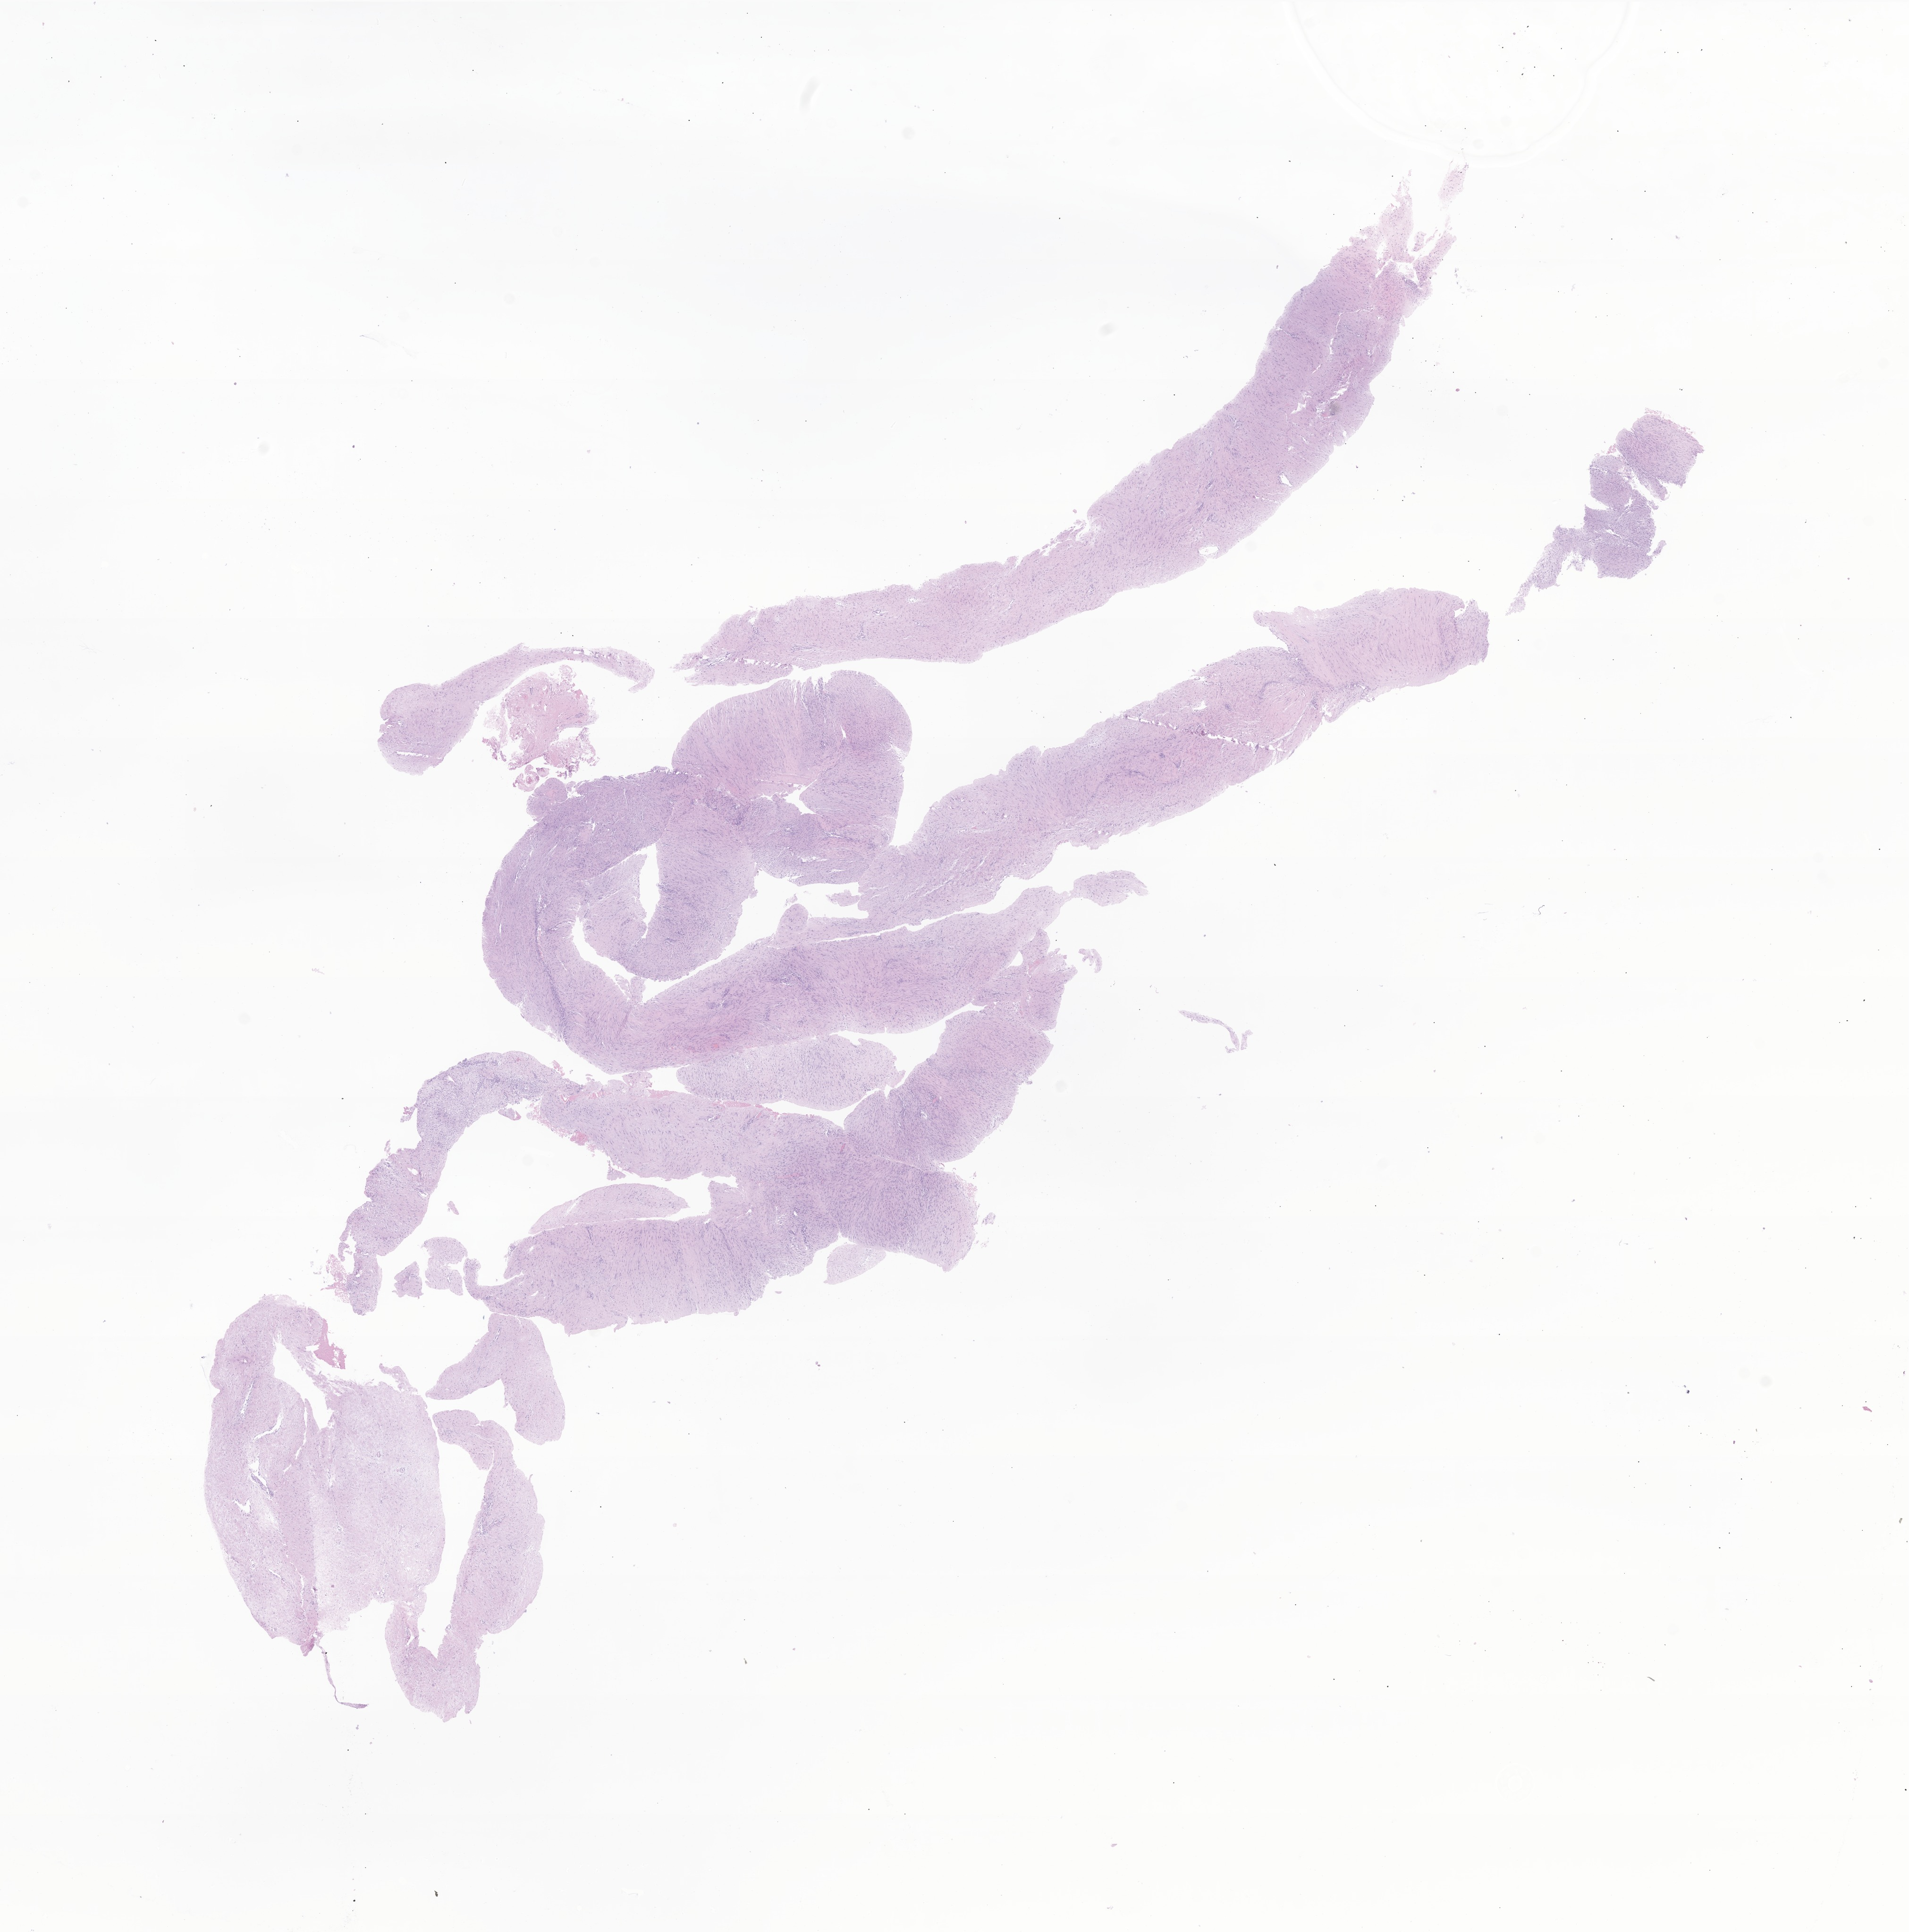
Whole-slide image, H&E stain of tumor tissue from the posterior mediastinum — a low-resolution overview of the entire scanned area, about 17.0 x 17.2 mm, FFPE section. Female patient, age 238 months (19 years 10 months).
Diagnosis: Aggressive fibromatosis.